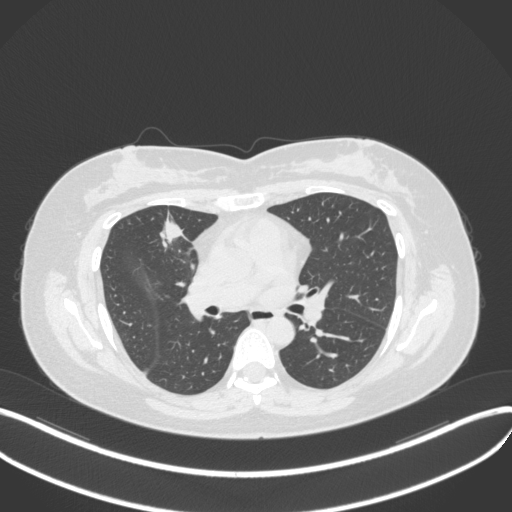
Chest CT, one axial slice; position 175 of 272 along the scan axis; 120 kVp; lung window (W 1500 / L -600 HU); 1 mm slice thickness; 512 × 512 image matrix. Patient: female, 42 years. Case-level facts recorded for this patient, not image findings: clinical TNM (as recorded): T1b N0 M0.
Structures marked on this image (bounding box drawn by a radiologist):
- lung tumour (recorded histology: adenocarcinoma): box from (x=152, y=217) to (x=190, y=251) px